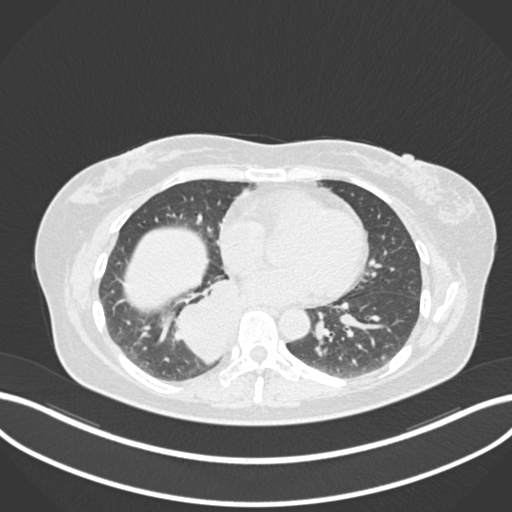
Chest CT, one axial slice. Slice 563 of 677 in the series (ordered by position). Reconstruction kernel B30f. Lung window (W 1500 / L -600 HU). 1 mm slice thickness. 512 × 512 image matrix. Female patient, age 54 years. From the clinical record (not read from this slice): clinical TNM (as recorded): T4 N0 M0.
Structures marked on this image (bounding box drawn by a radiologist):
- lung tumour (recorded histology: adenocarcinoma): box from (x=167, y=273) to (x=250, y=368) px